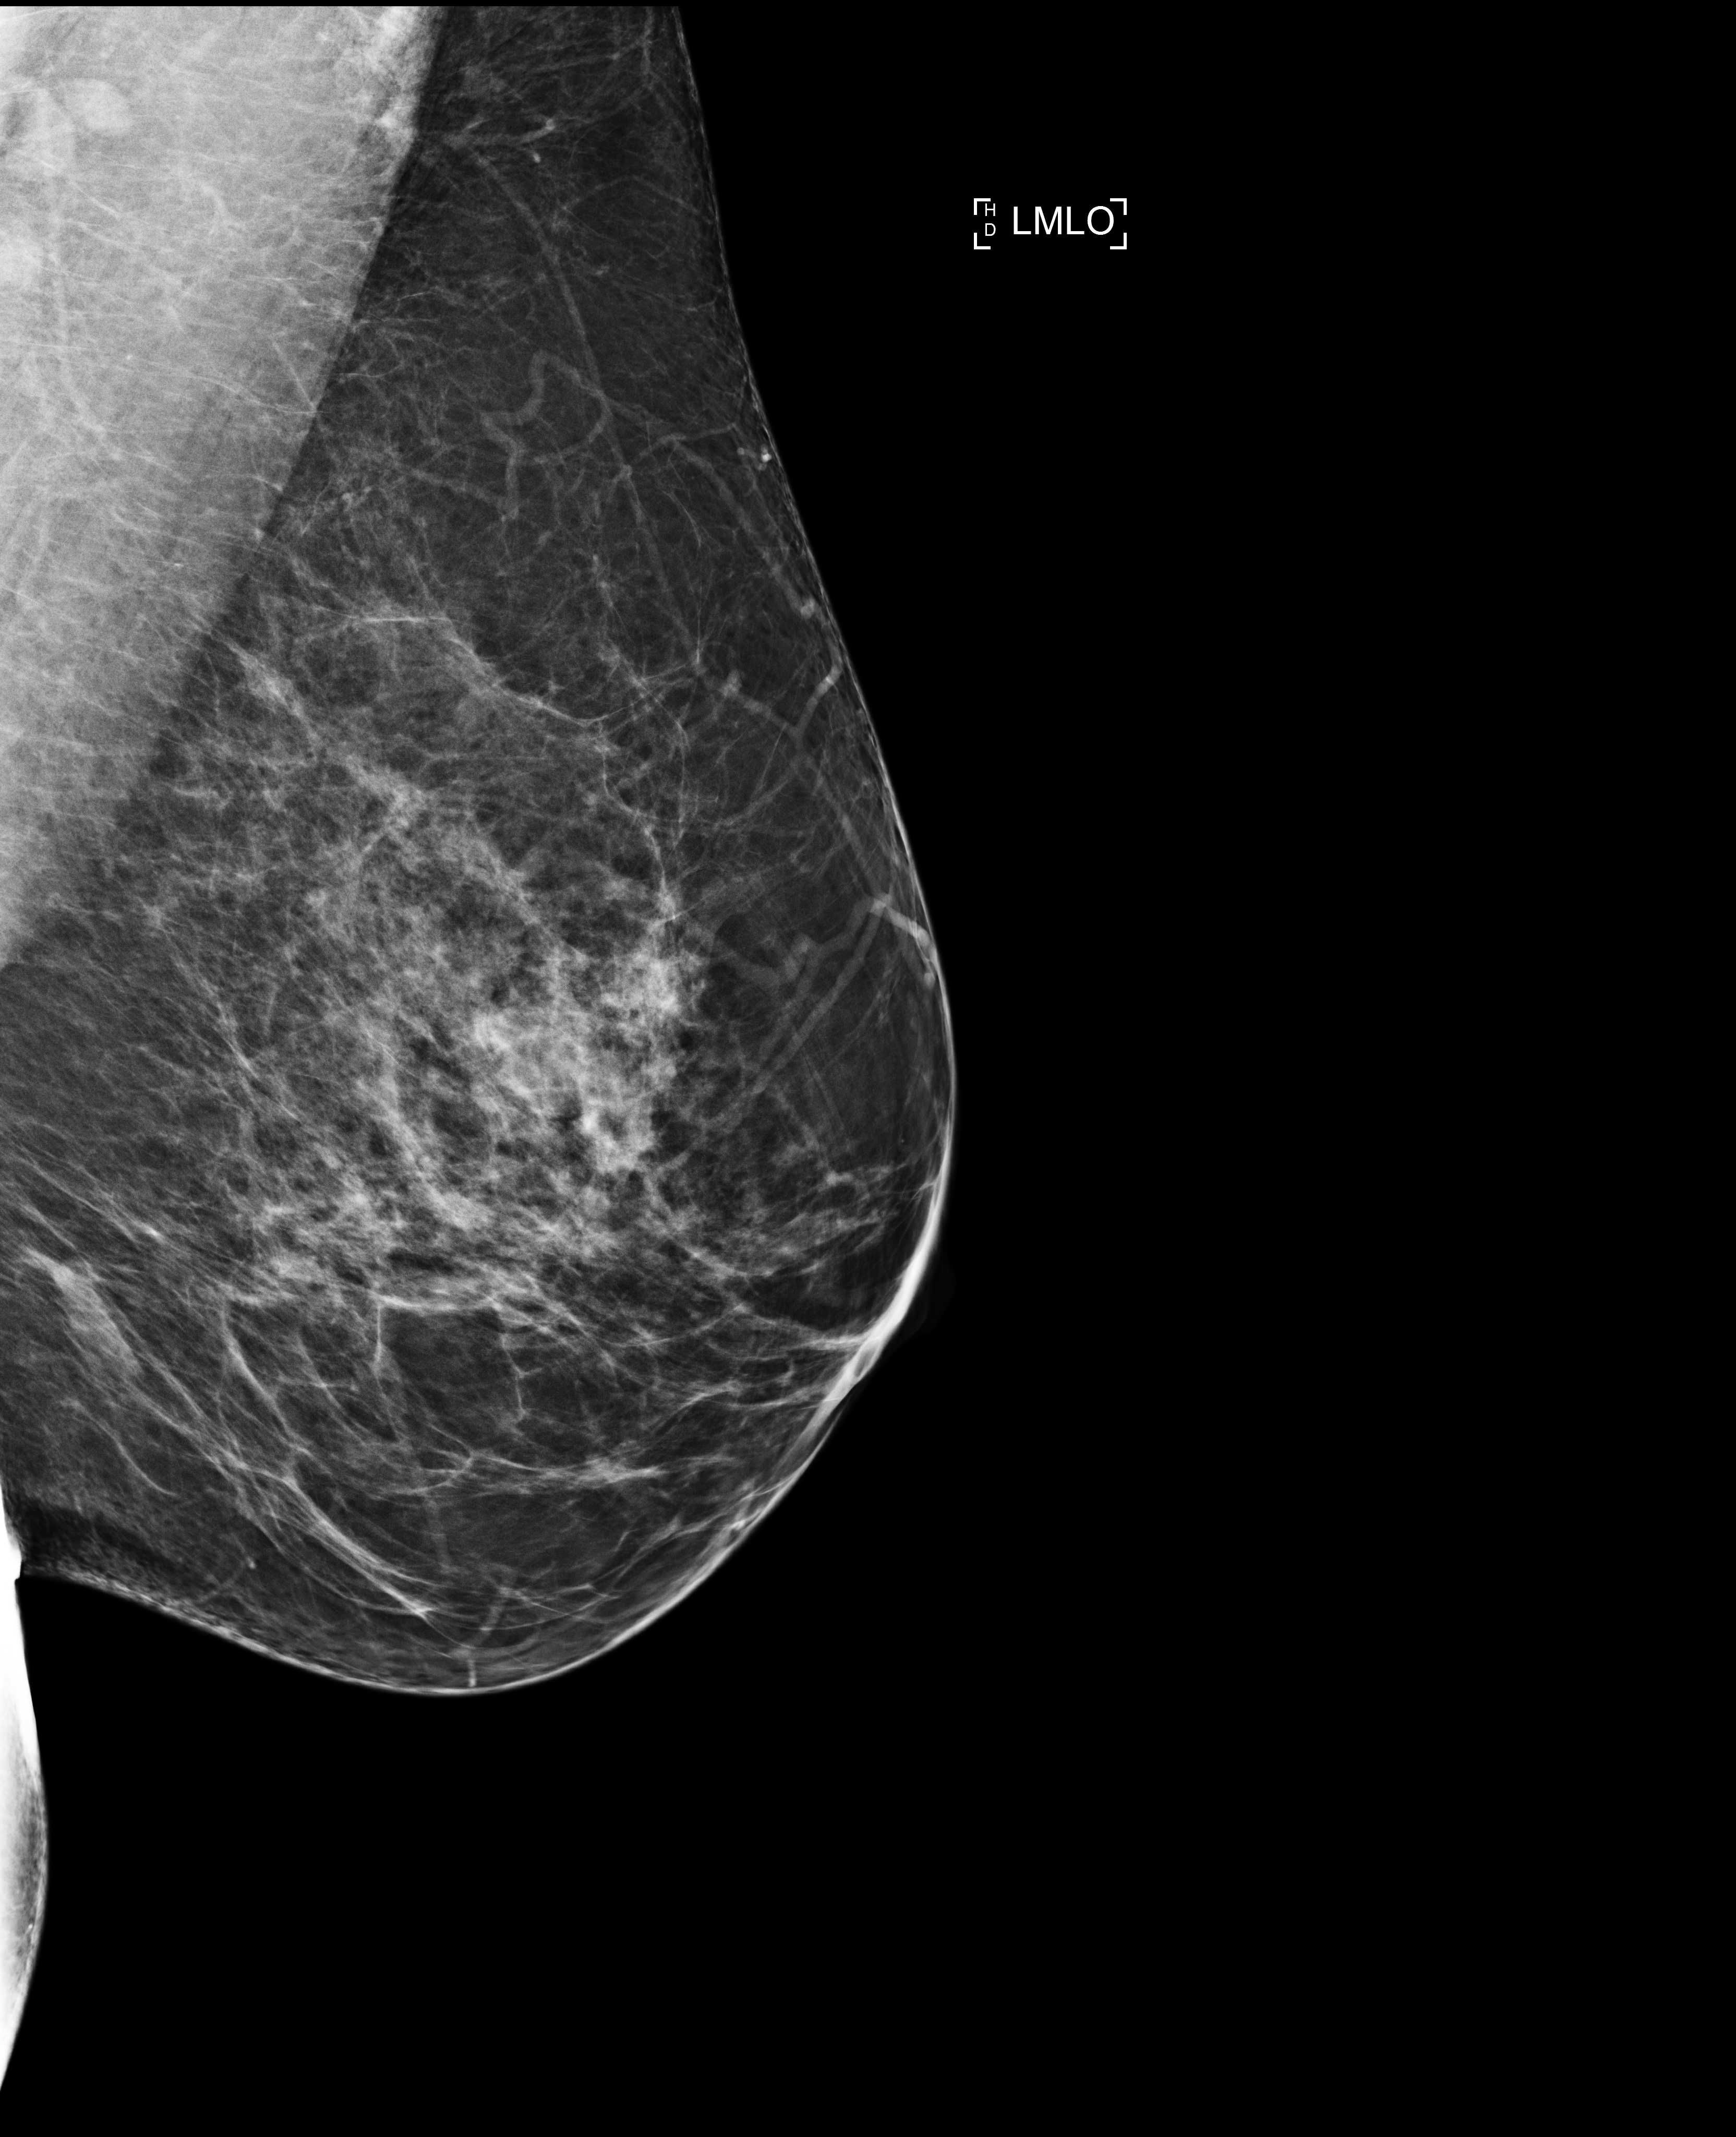
Screening examination; compressed breast thickness 70 mm; system: Selenia Dimensions. Patient aged 51 years (female).
Image type: full-field digital mammogram. Breast: left. Projection: MLO view.